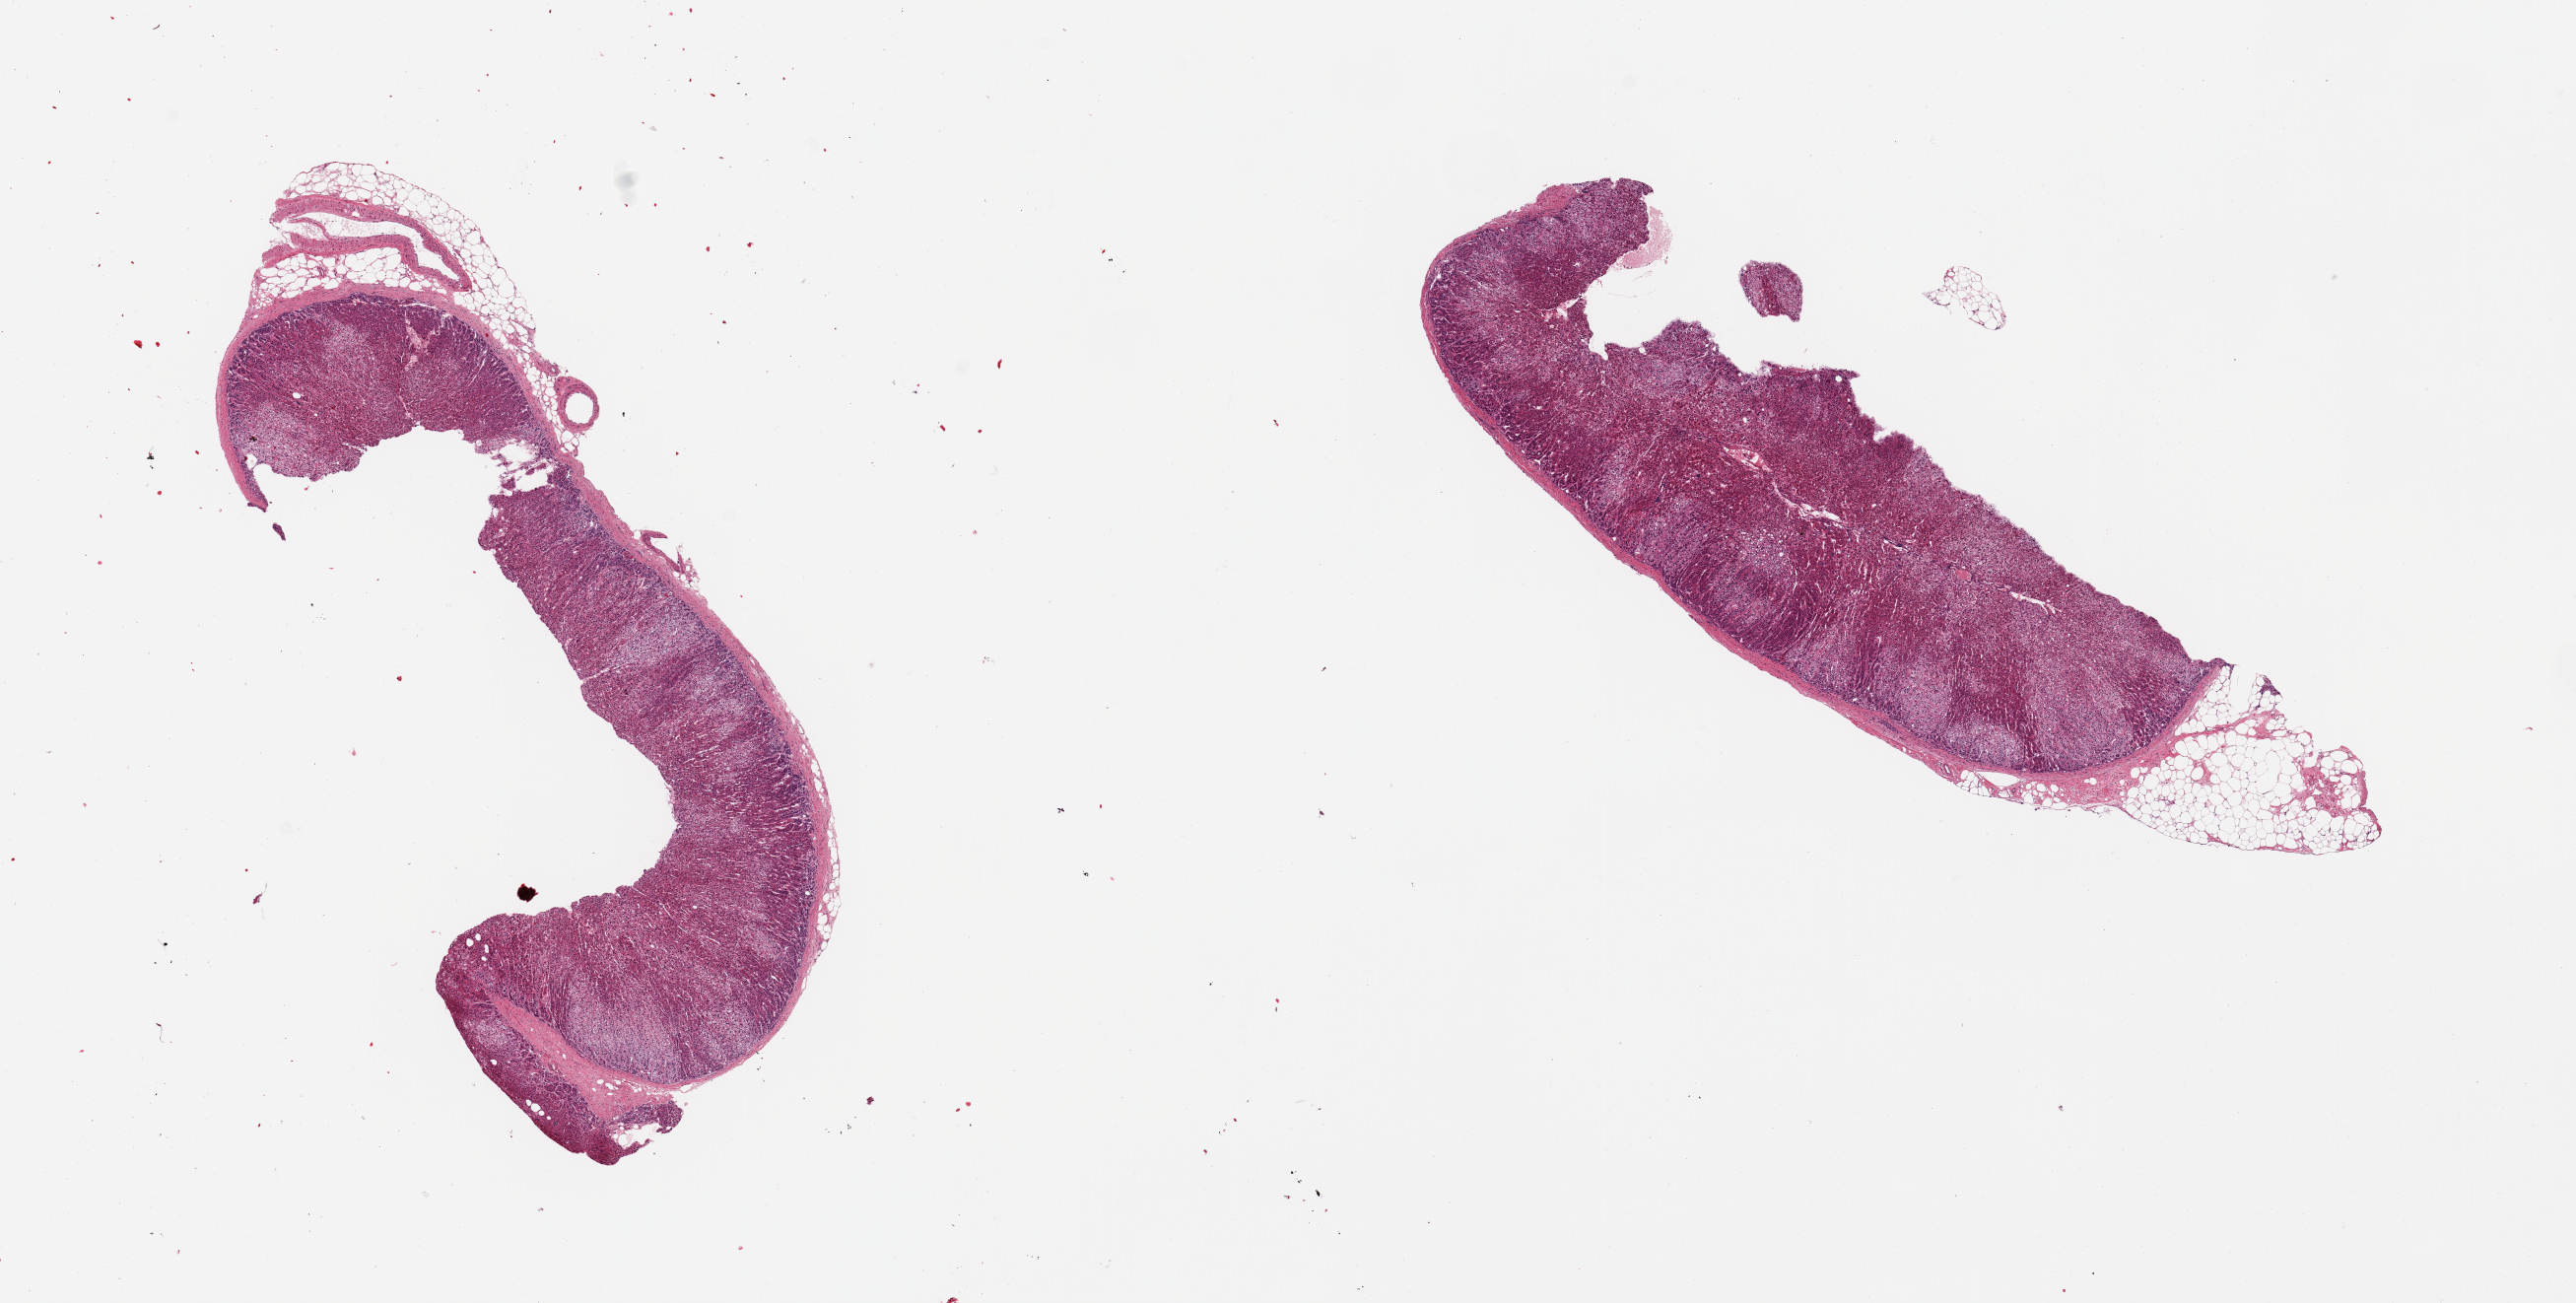
Digitized haematoxylin and eosin-stained section — shown as a low-resolution overview of the whole scanned area (about 20.7 x 10.5 mm); PAXgene-fixed, paraffin-embedded tissue; section of adrenal gland (target tissue); tissue donor sample. Male donor.
Review note (as recorded): 2 pieces; 20 & 10% external fat at edges.